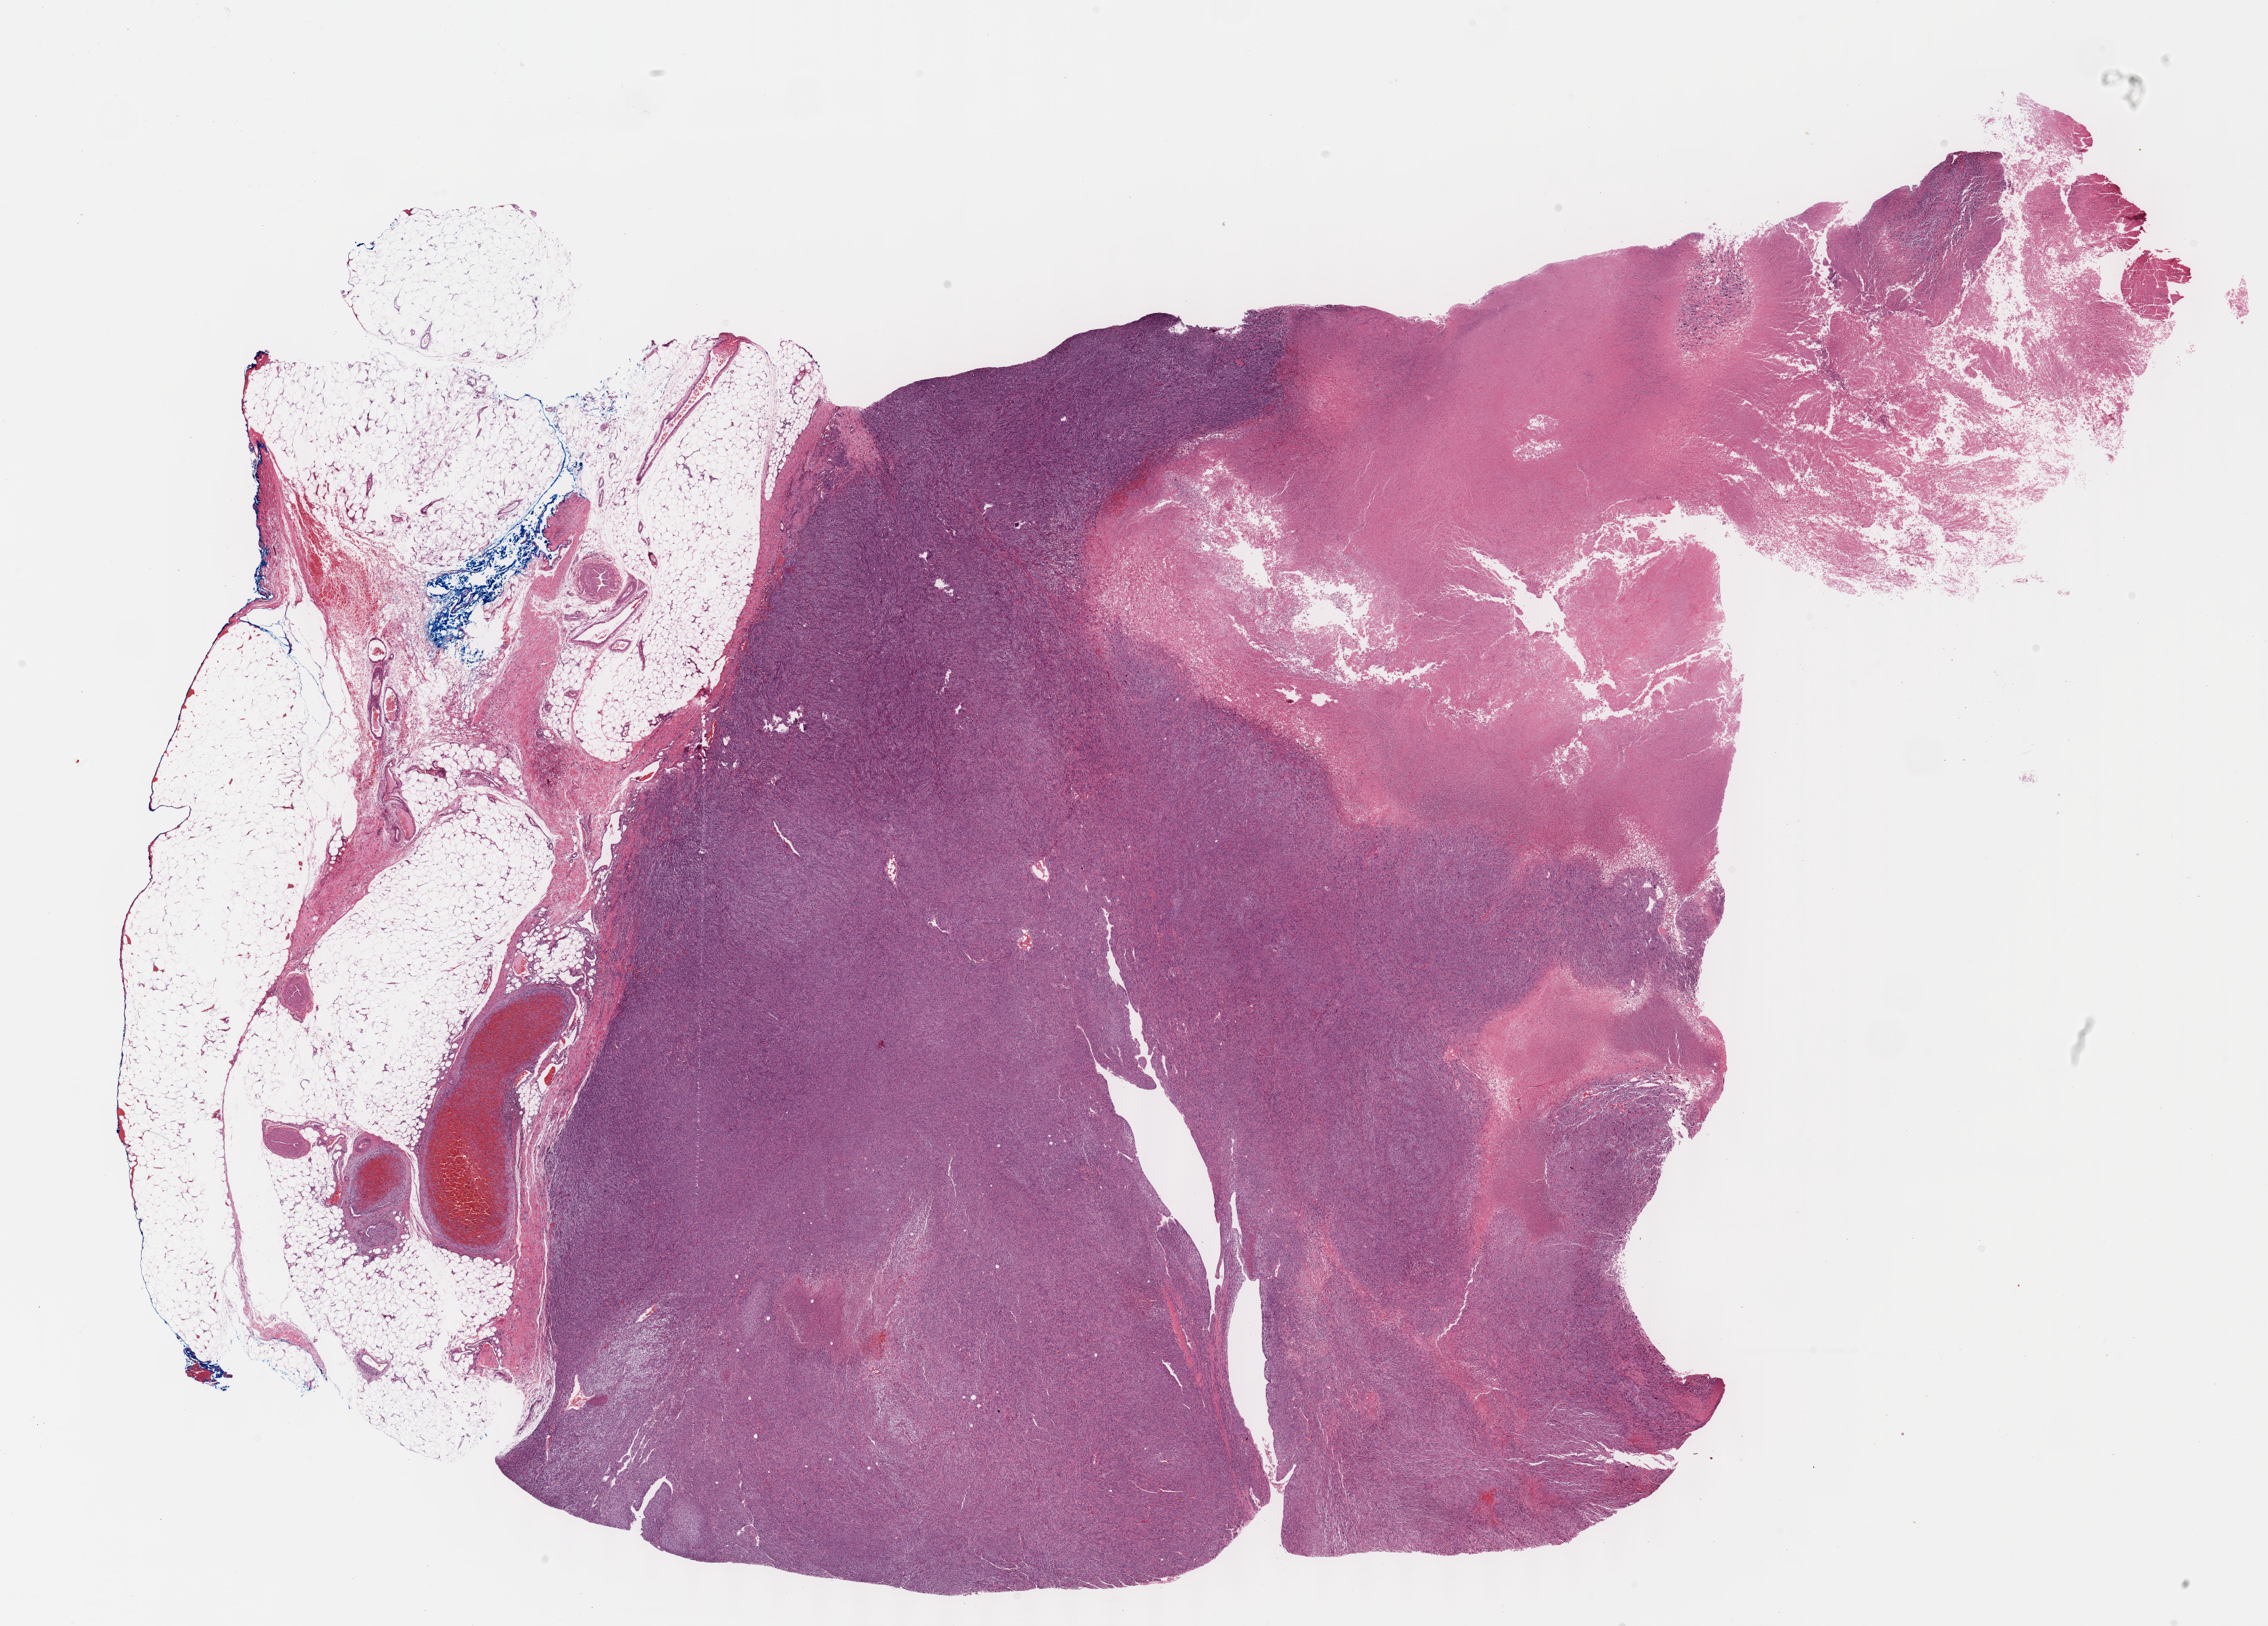
Digitized Hematoxylin and eosin (H&E) stained tissue section (whole slide) — shown as a low-resolution overview of the whole scanned area (about 27.2 x 19.5 mm, from a 40x scan); formalin-fixed paraffin-embedded (FFPE) diagnostic section; connective, subcutaneous and other soft tissues, primary tumour sample. Female patient; age at initial diagnosis 68 years.
Diagnosis: Fibromyxosarcoma (connective, subcutaneous and other soft tissues of lower limb and hip).